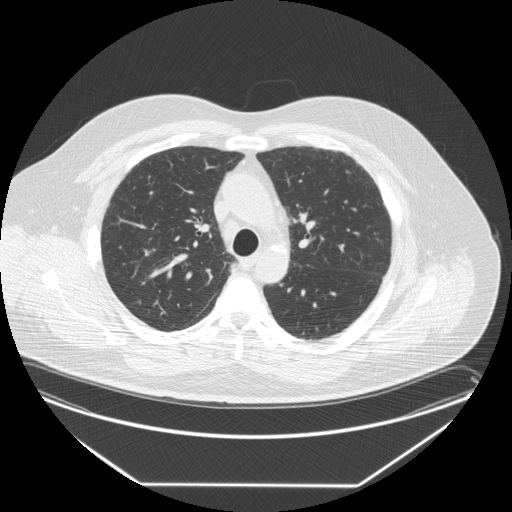
Low-dose screening chest CT, one axial slice. Position 190 of 258 along the scan axis. 120 kVp. Lung window (W 1500 / L -600 HU). 512 × 512 image matrix.
Structures marked on this image (expert manual segmentation):
- lesion 1 (tumor, upper lobe of right lung): bounding box <231,263,239,271> (left, top, right, bottom; pixels)